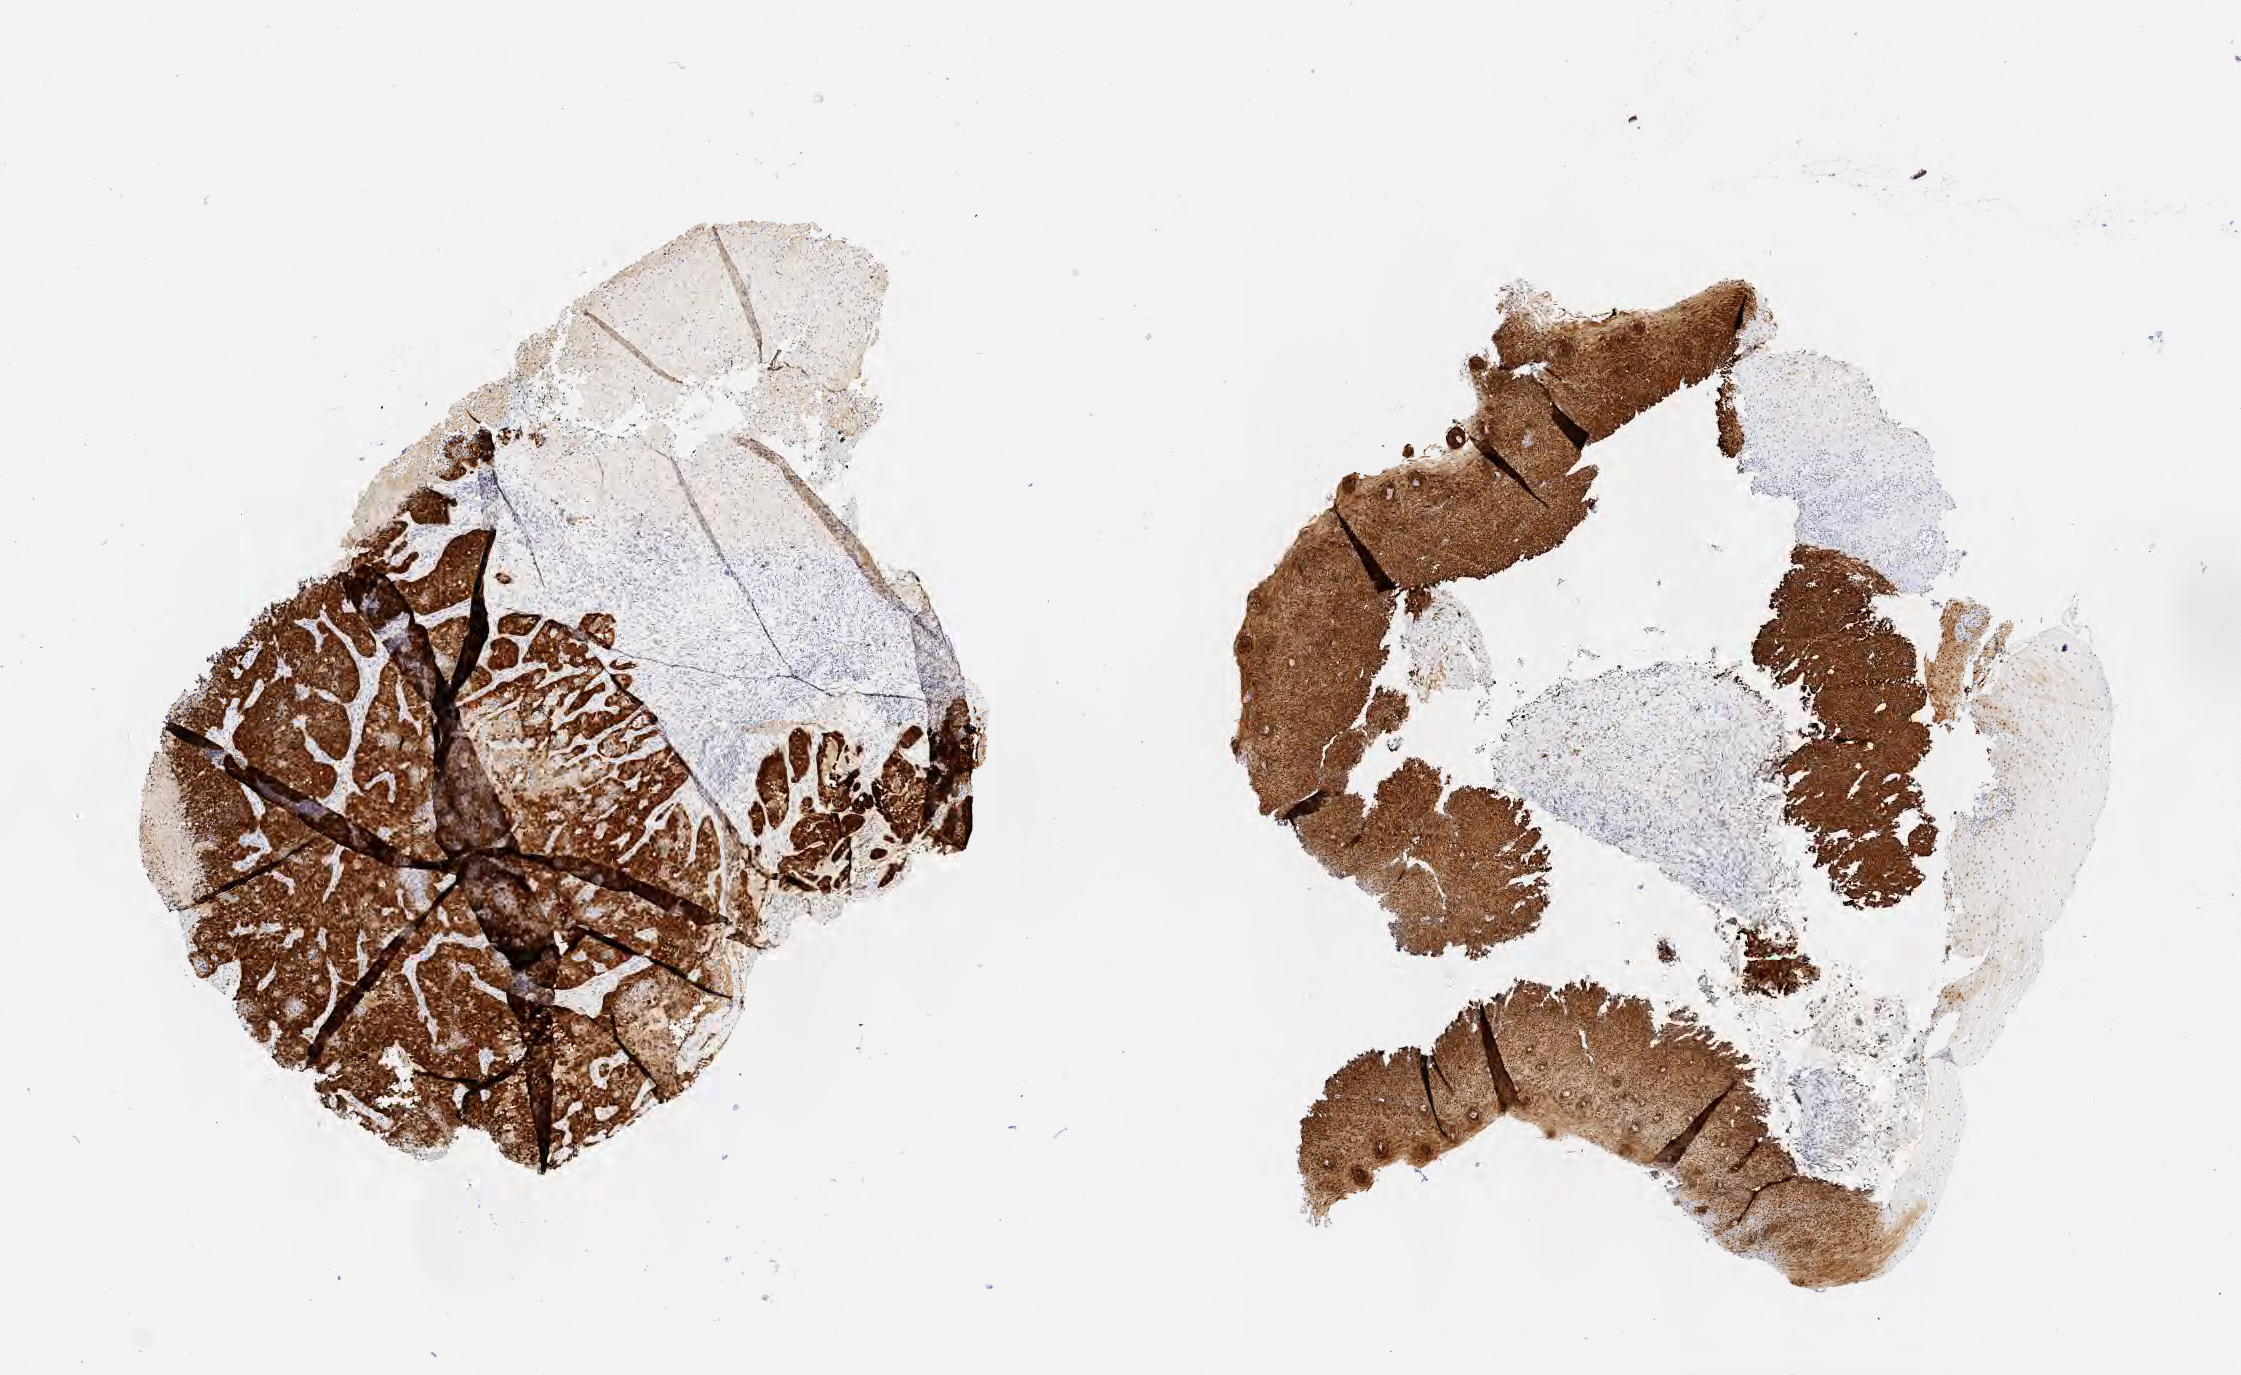
Whole-slide image, immunohistochemical stain for p16 (p16INK4a) — low-resolution overview of the scanned area, about 9.1 x 5.6 mm; tumor tissue; site: cervix. Female patient, age 57 years.
* histologic diagnosis: Squamous cell carcinoma, large cell, nonkeratinizing, NOS